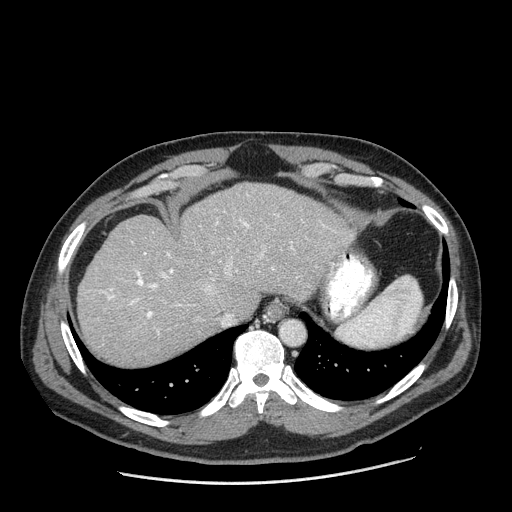
Contrast-enhanced abdominal CT (liver protocol), one axial slice; slice 153 of 198 in the series (ordered by position); reconstruction kernel STANDARD; 120 kVp; one of 2 acquisitions stored at this slice position; soft-tissue window (W 400 / L 40 HU); 2.5 mm slice thickness; 512 × 512 image matrix. Case-level facts recorded for this patient, not image findings: diagnosis: hepatocellular carcinoma (patient treated with transarterial chemoembolisation; whether this scan precedes or follows treatment is not stated here); TNM stage (as recorded): Stage-II; Child-Pugh class: A; tumour differentiation: moderately differentiated.
Outlined on this slice (semi-automatic segmentation, software-assisted and operator-edited):
- abdominal aorta: bounding box <281,321,303,344> (left, top, right, bottom; pixels)
- liver parenchyma outside the tumour (the mass and vessels are separate outlines, so this box may not span the whole liver): <78,182,355,364>
- liver vessels: <101,211,333,334>